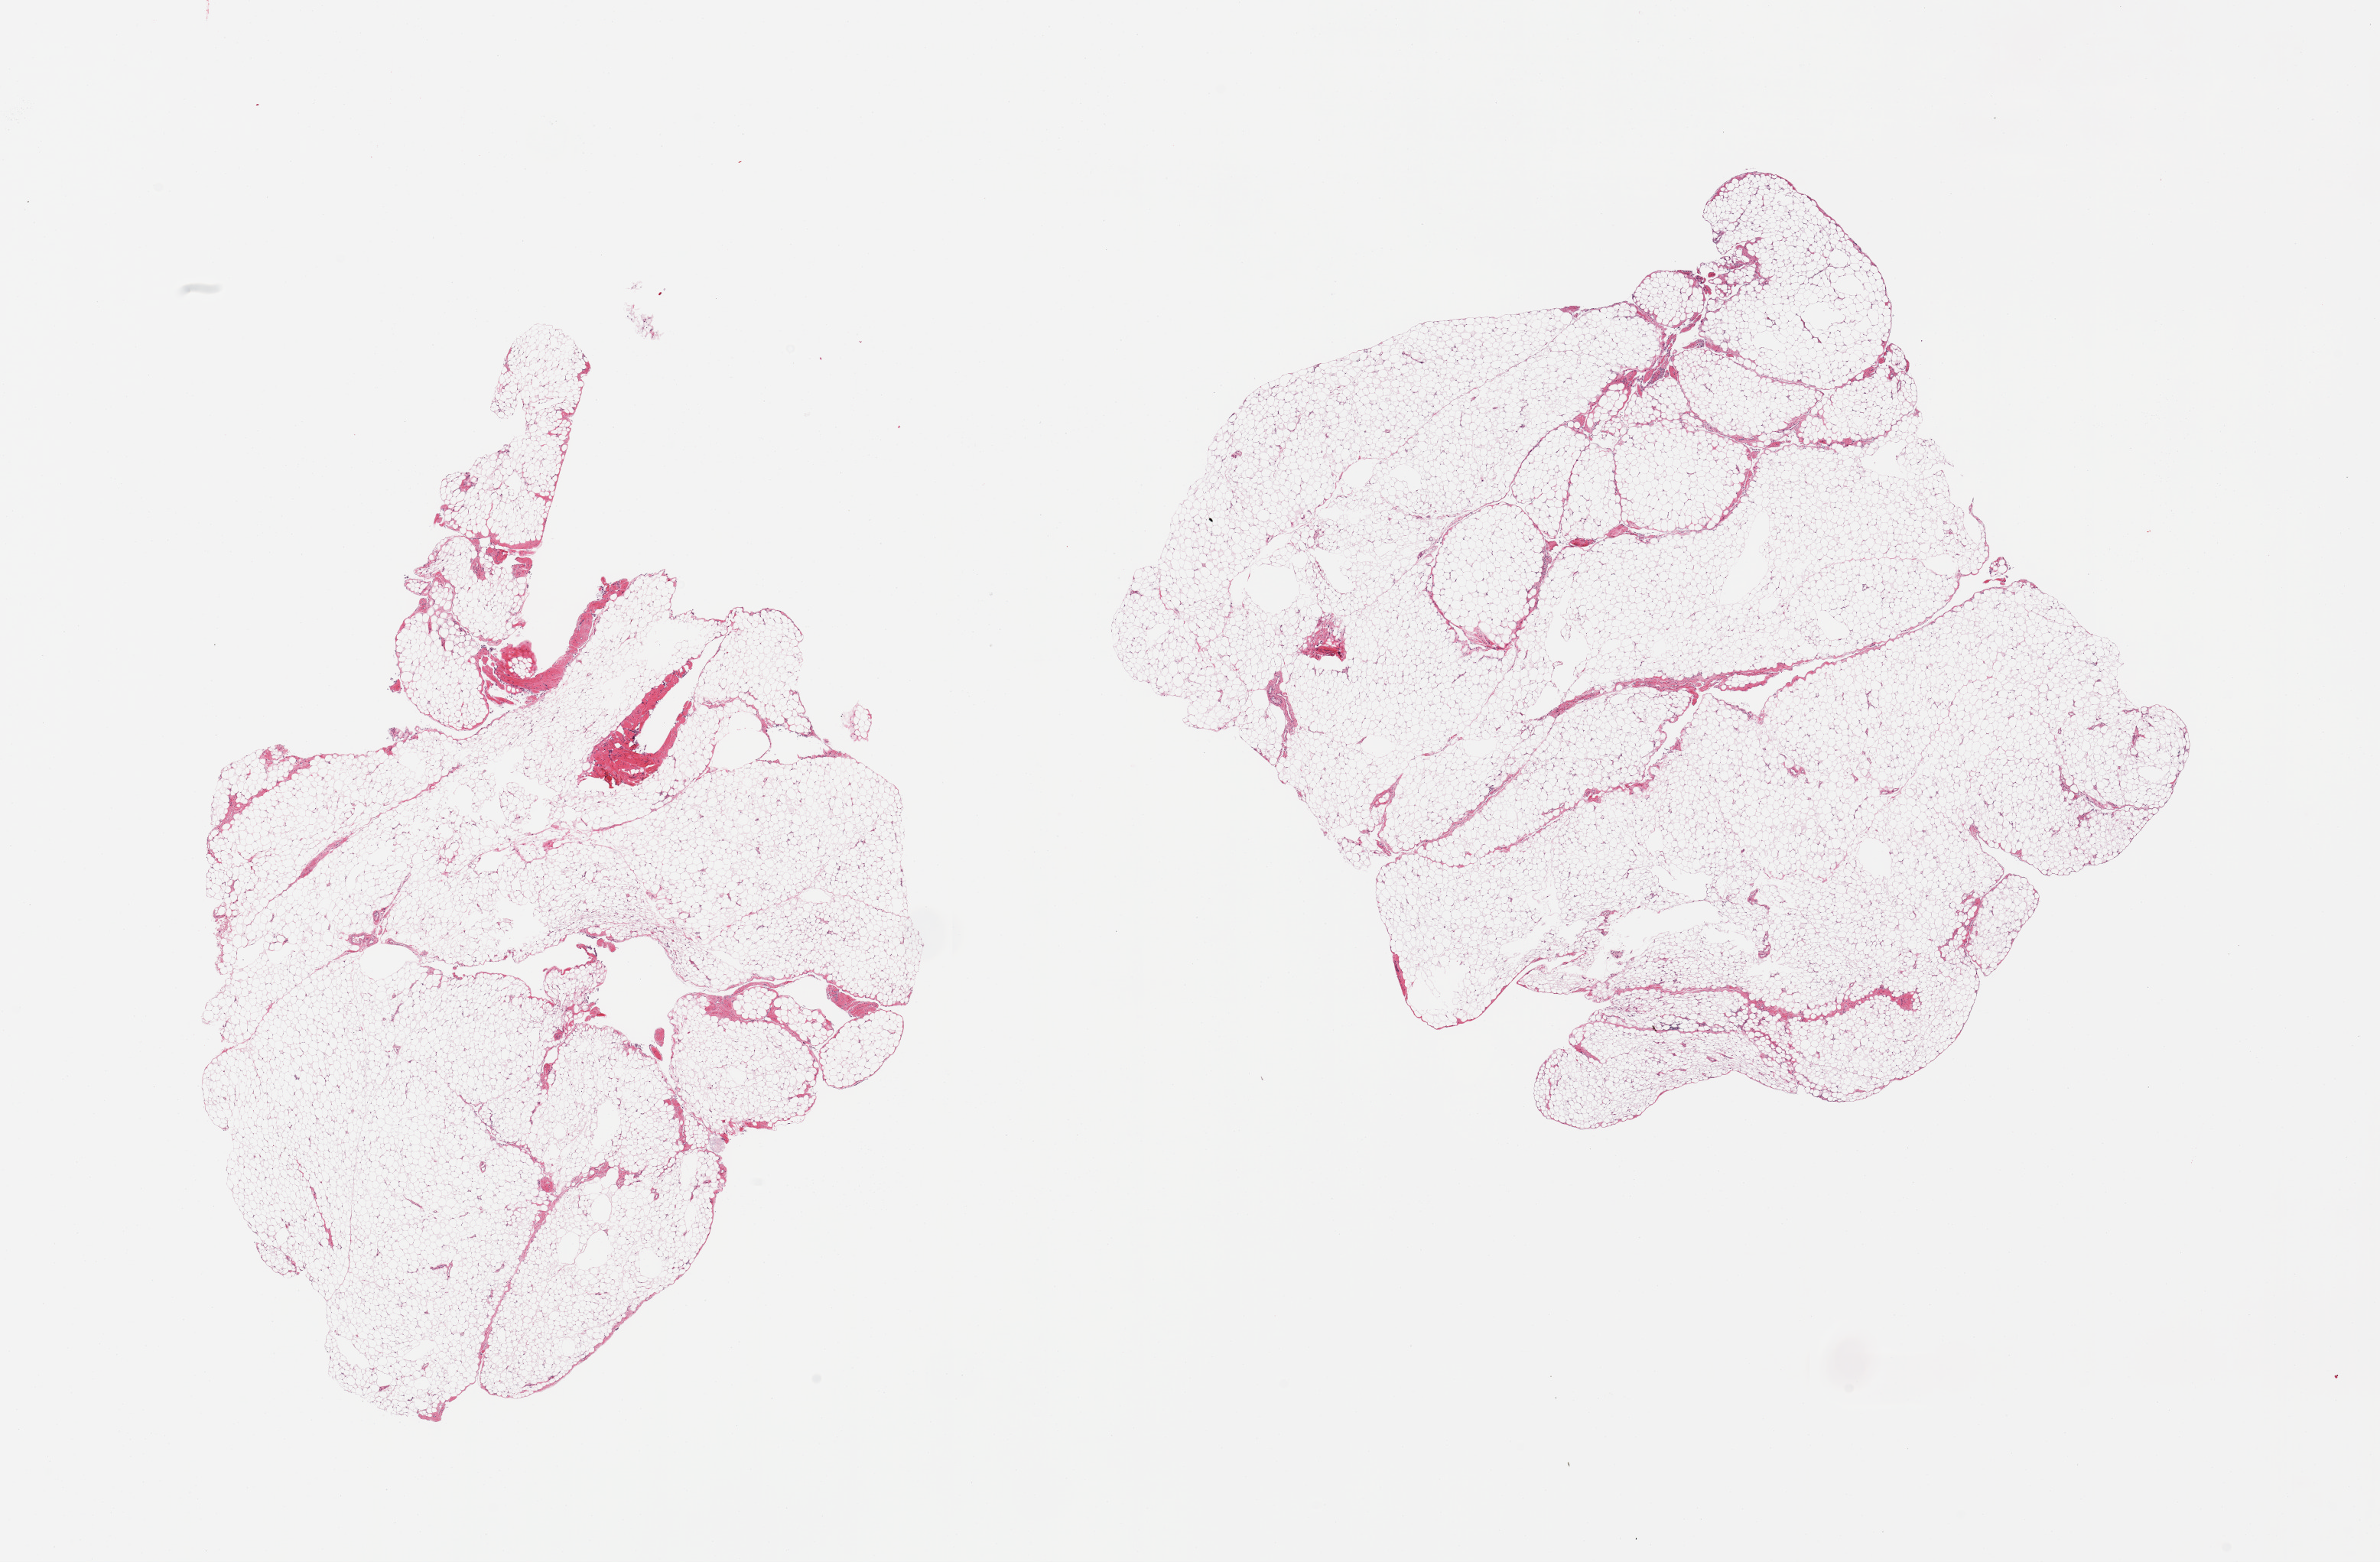
H&E whole-slide image, brightfield, low-resolution overview of the scanned area, about 24.6 x 16.2 mm. PAXgene-fixed paraffin-embedded (PFPE) section. Section of omentum (target tissue). Tissue donor sample. Donor: female.
* review note (as recorded): 2 pieces; mature fat